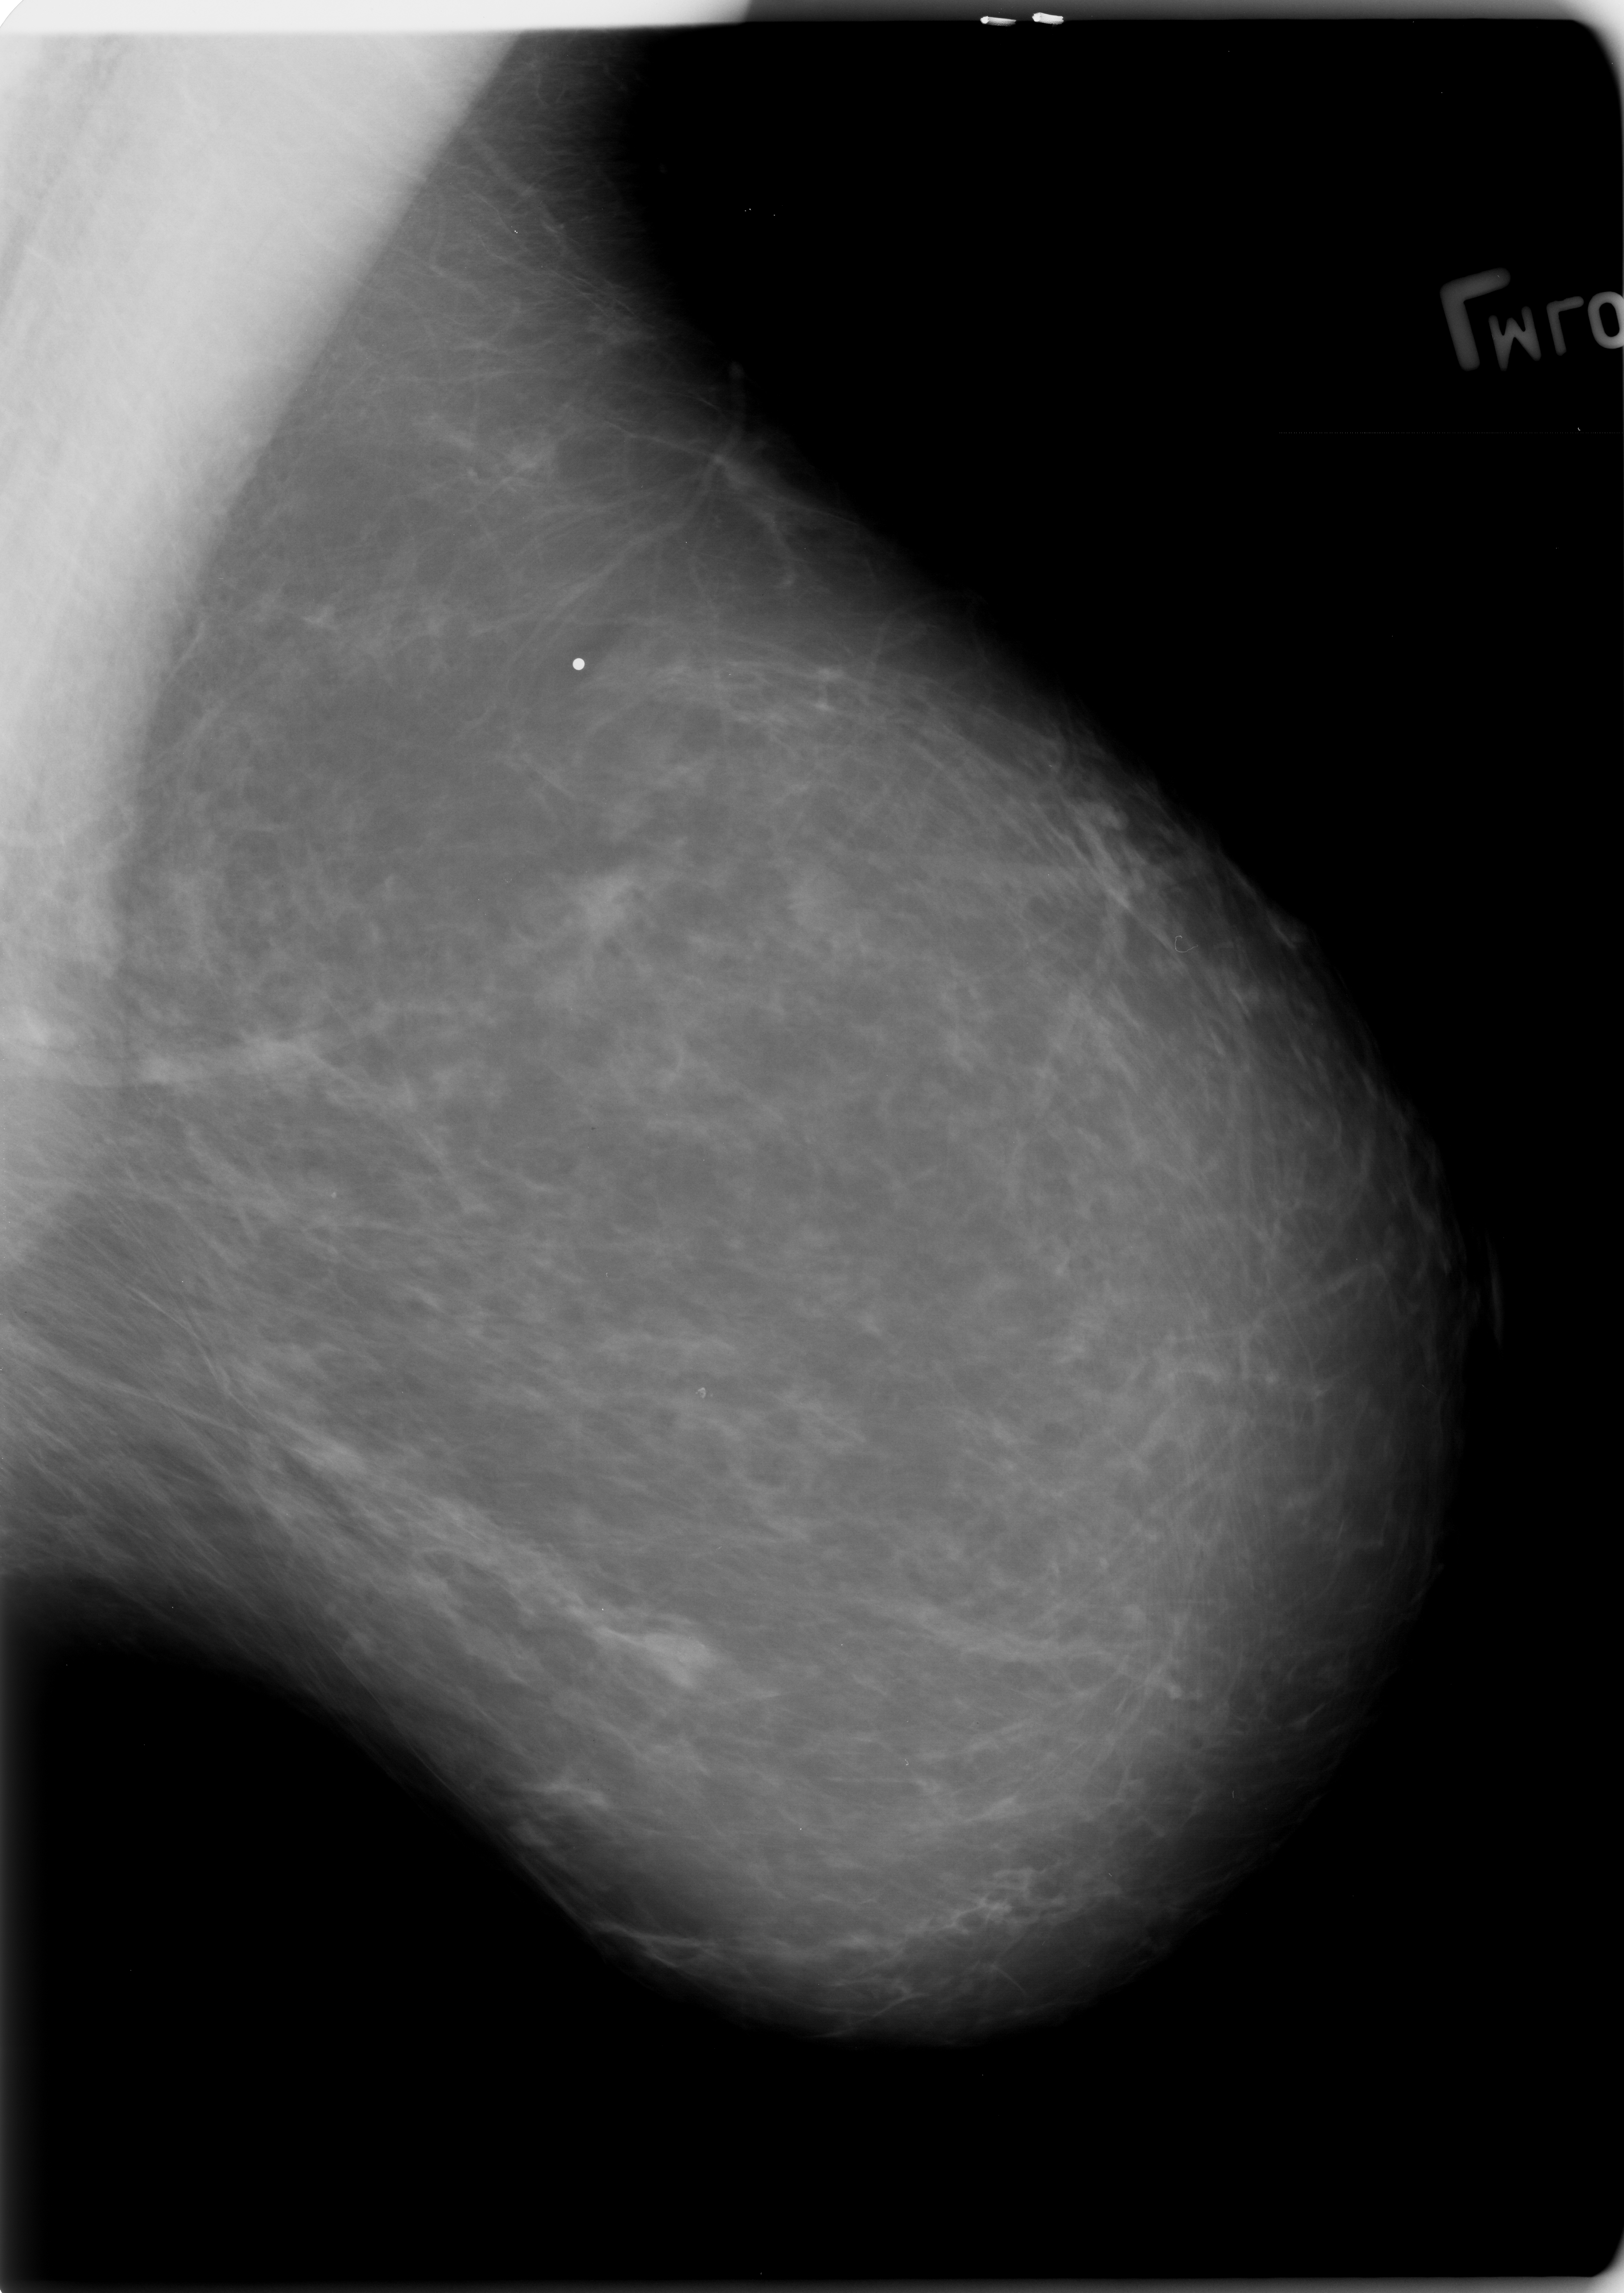
Mammogram (digitized film). Left breast. MLO view. Breast composition: scattered fibroglandular densities (BI-RADS density category 2 of 4). 1624 × 2293 image matrix.
Marked abnormalities (boxes around the expert regions of interest):
- calcifications, morphology amorphous, distribution clustered; BI-RADS assessment category 4; pathology (as recorded): benign: bounding box [x1, y1, x2, y2] px = [609, 1630, 717, 1697]